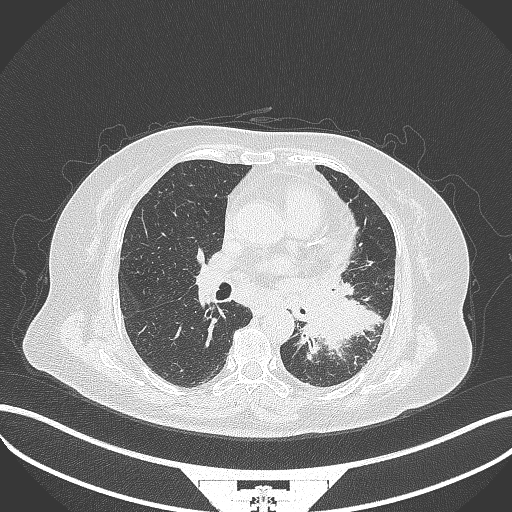
Chest CT, one axial slice. Slice 181 of 322 in the series (ordered by position). Reconstruction kernel B70f. Lung window (W 1500 / L -600 HU). 512 × 512 image matrix. Patient: female, 69 years. From the clinical record (not read from this slice): clinical TNM (as recorded): T2b N3 M1.
Outlined on this slice (bounding box drawn by a radiologist):
- lung tumour (recorded histology: adenocarcinoma): bounding box <296,285,364,358> (left, top, right, bottom; pixels)